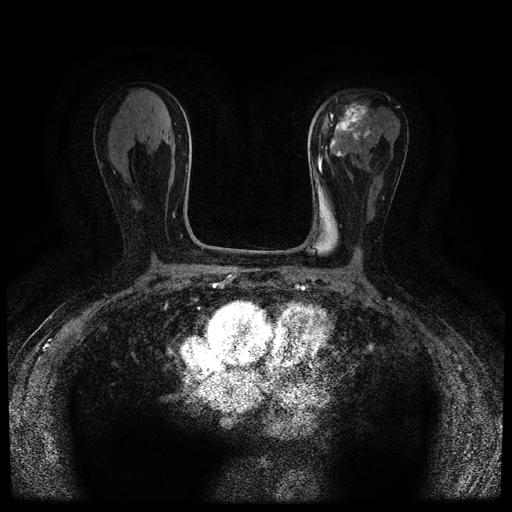
Breast MRI (dynamic contrast-enhanced, multi-phase), one axial slice. Dynamic contrast-enhanced series, time point 2 of 5 at this slice position (early post-contrast). 1.5 T. TE 2.7 ms, TR 5.4 ms. 2 mm slice thickness. 512 × 512 image matrix, field of view 320 × 320 mm. Patient: female, 80 years.
Annotated regions visible in this slice (semi-automatically segmented with operator editing):
- breast lesion (labelled 'tumour' in the annotation; benign lesions carry a separate 'benign' label): bounding box <323,103,371,157> (left, top, right, bottom; pixels)